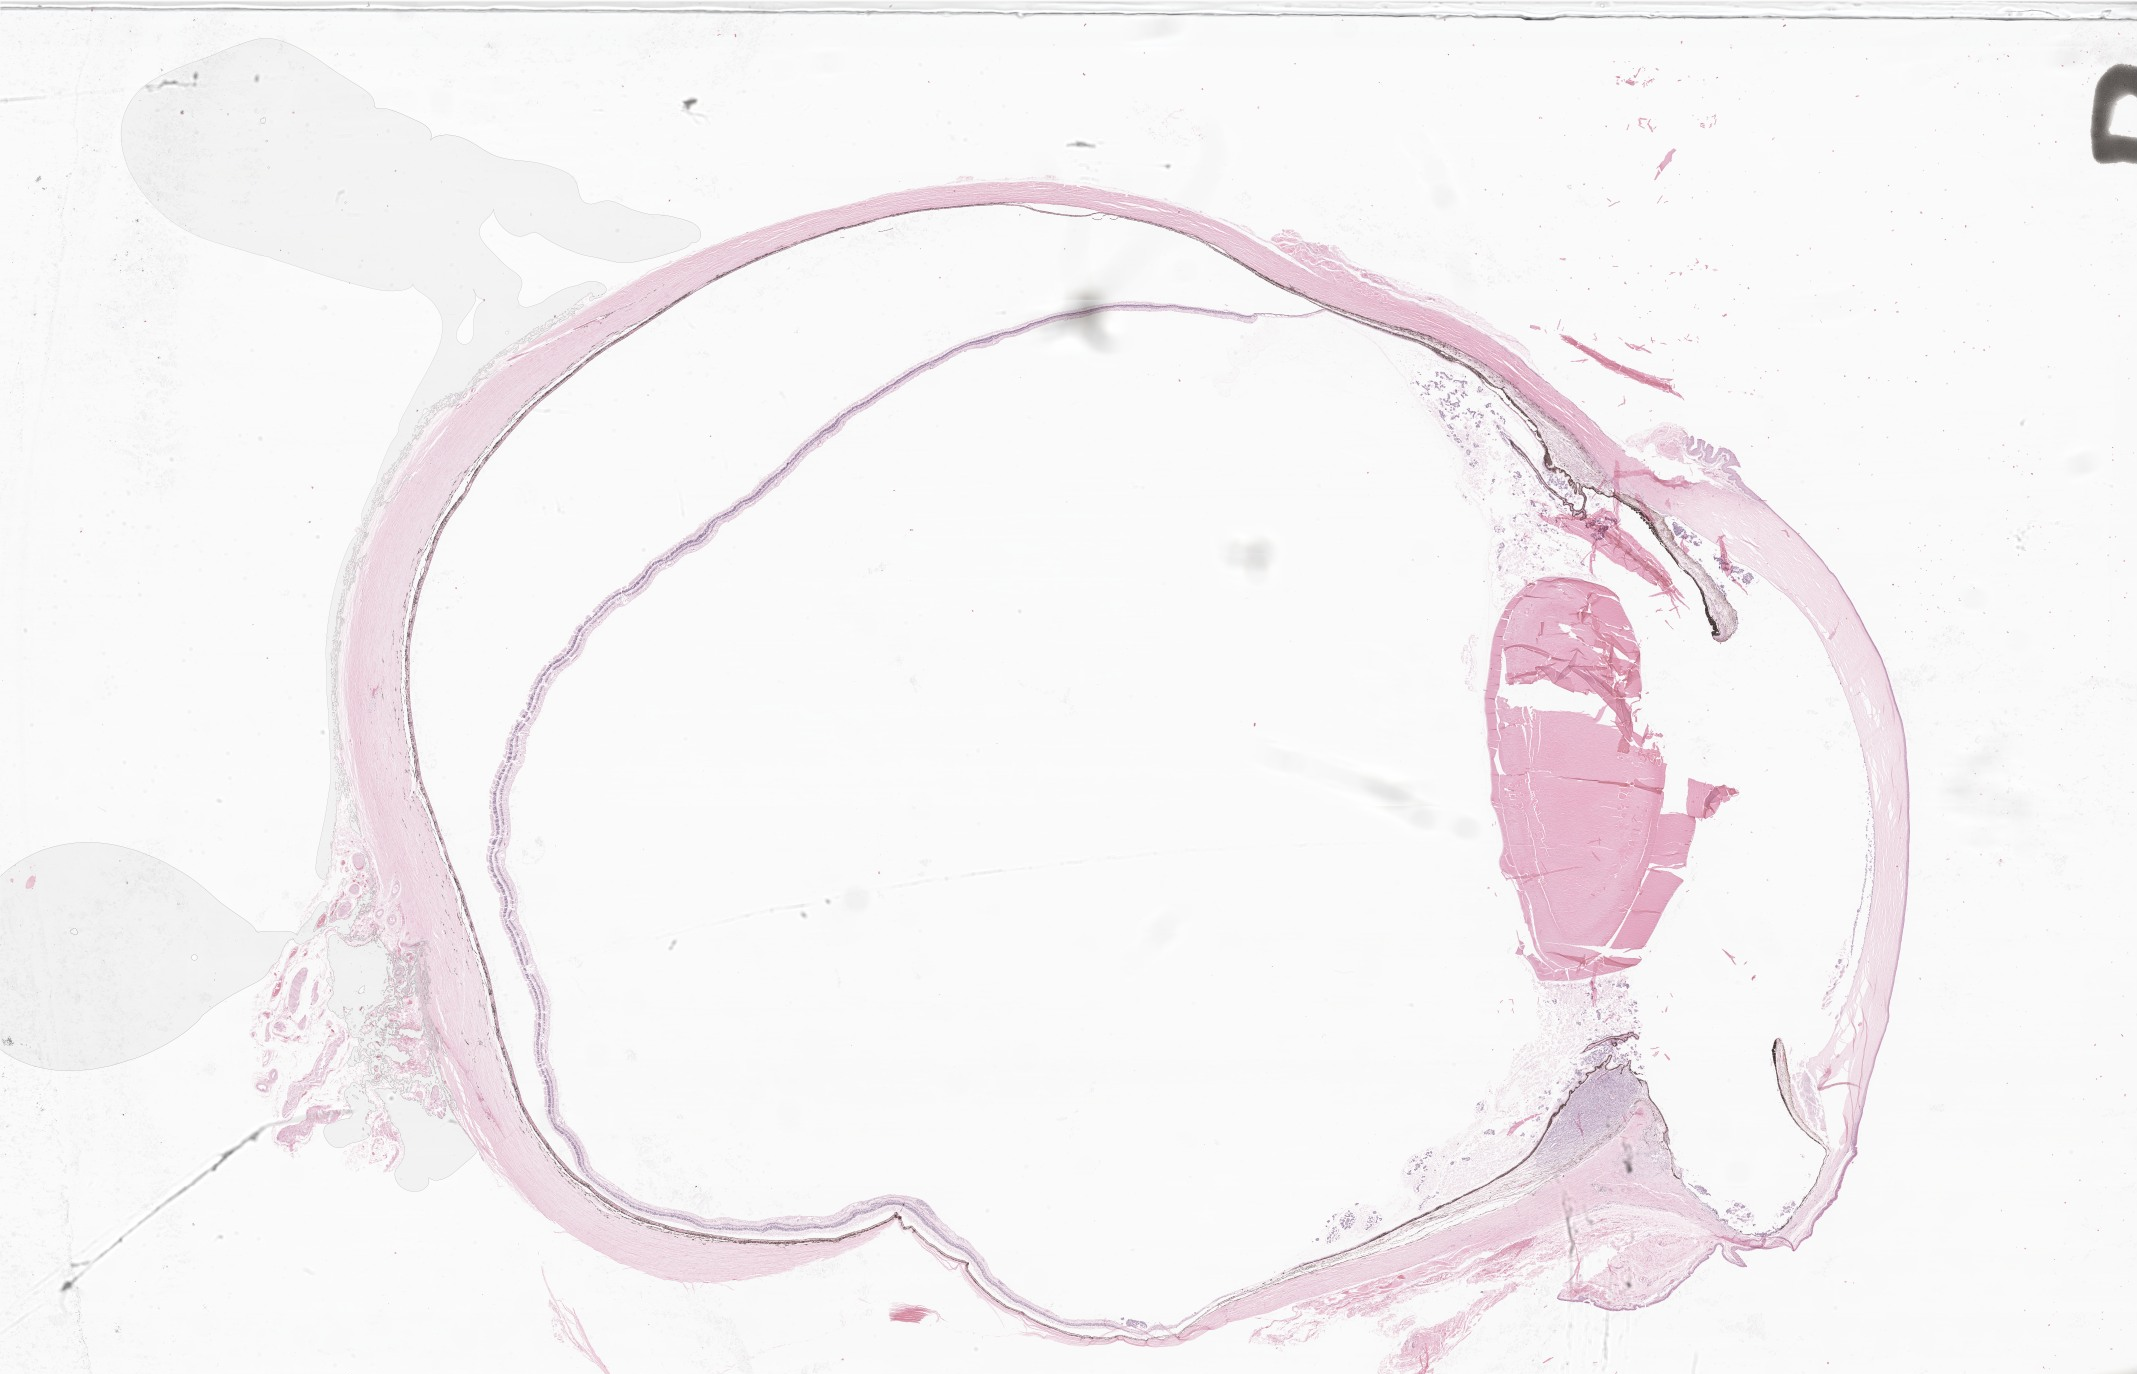
Digitized hematoxylin and eosin (H&E)-stained section of tumor tissue from the eye — whole scanned area (about 36.0 x 23.2 mm) shown as a low-resolution overview; formalin-fixed, paraffin-embedded (FFPE) tissue. Patient male; age 80 months (6 years 8 months).
• diagnosis: Retinoblastoma, diffuse